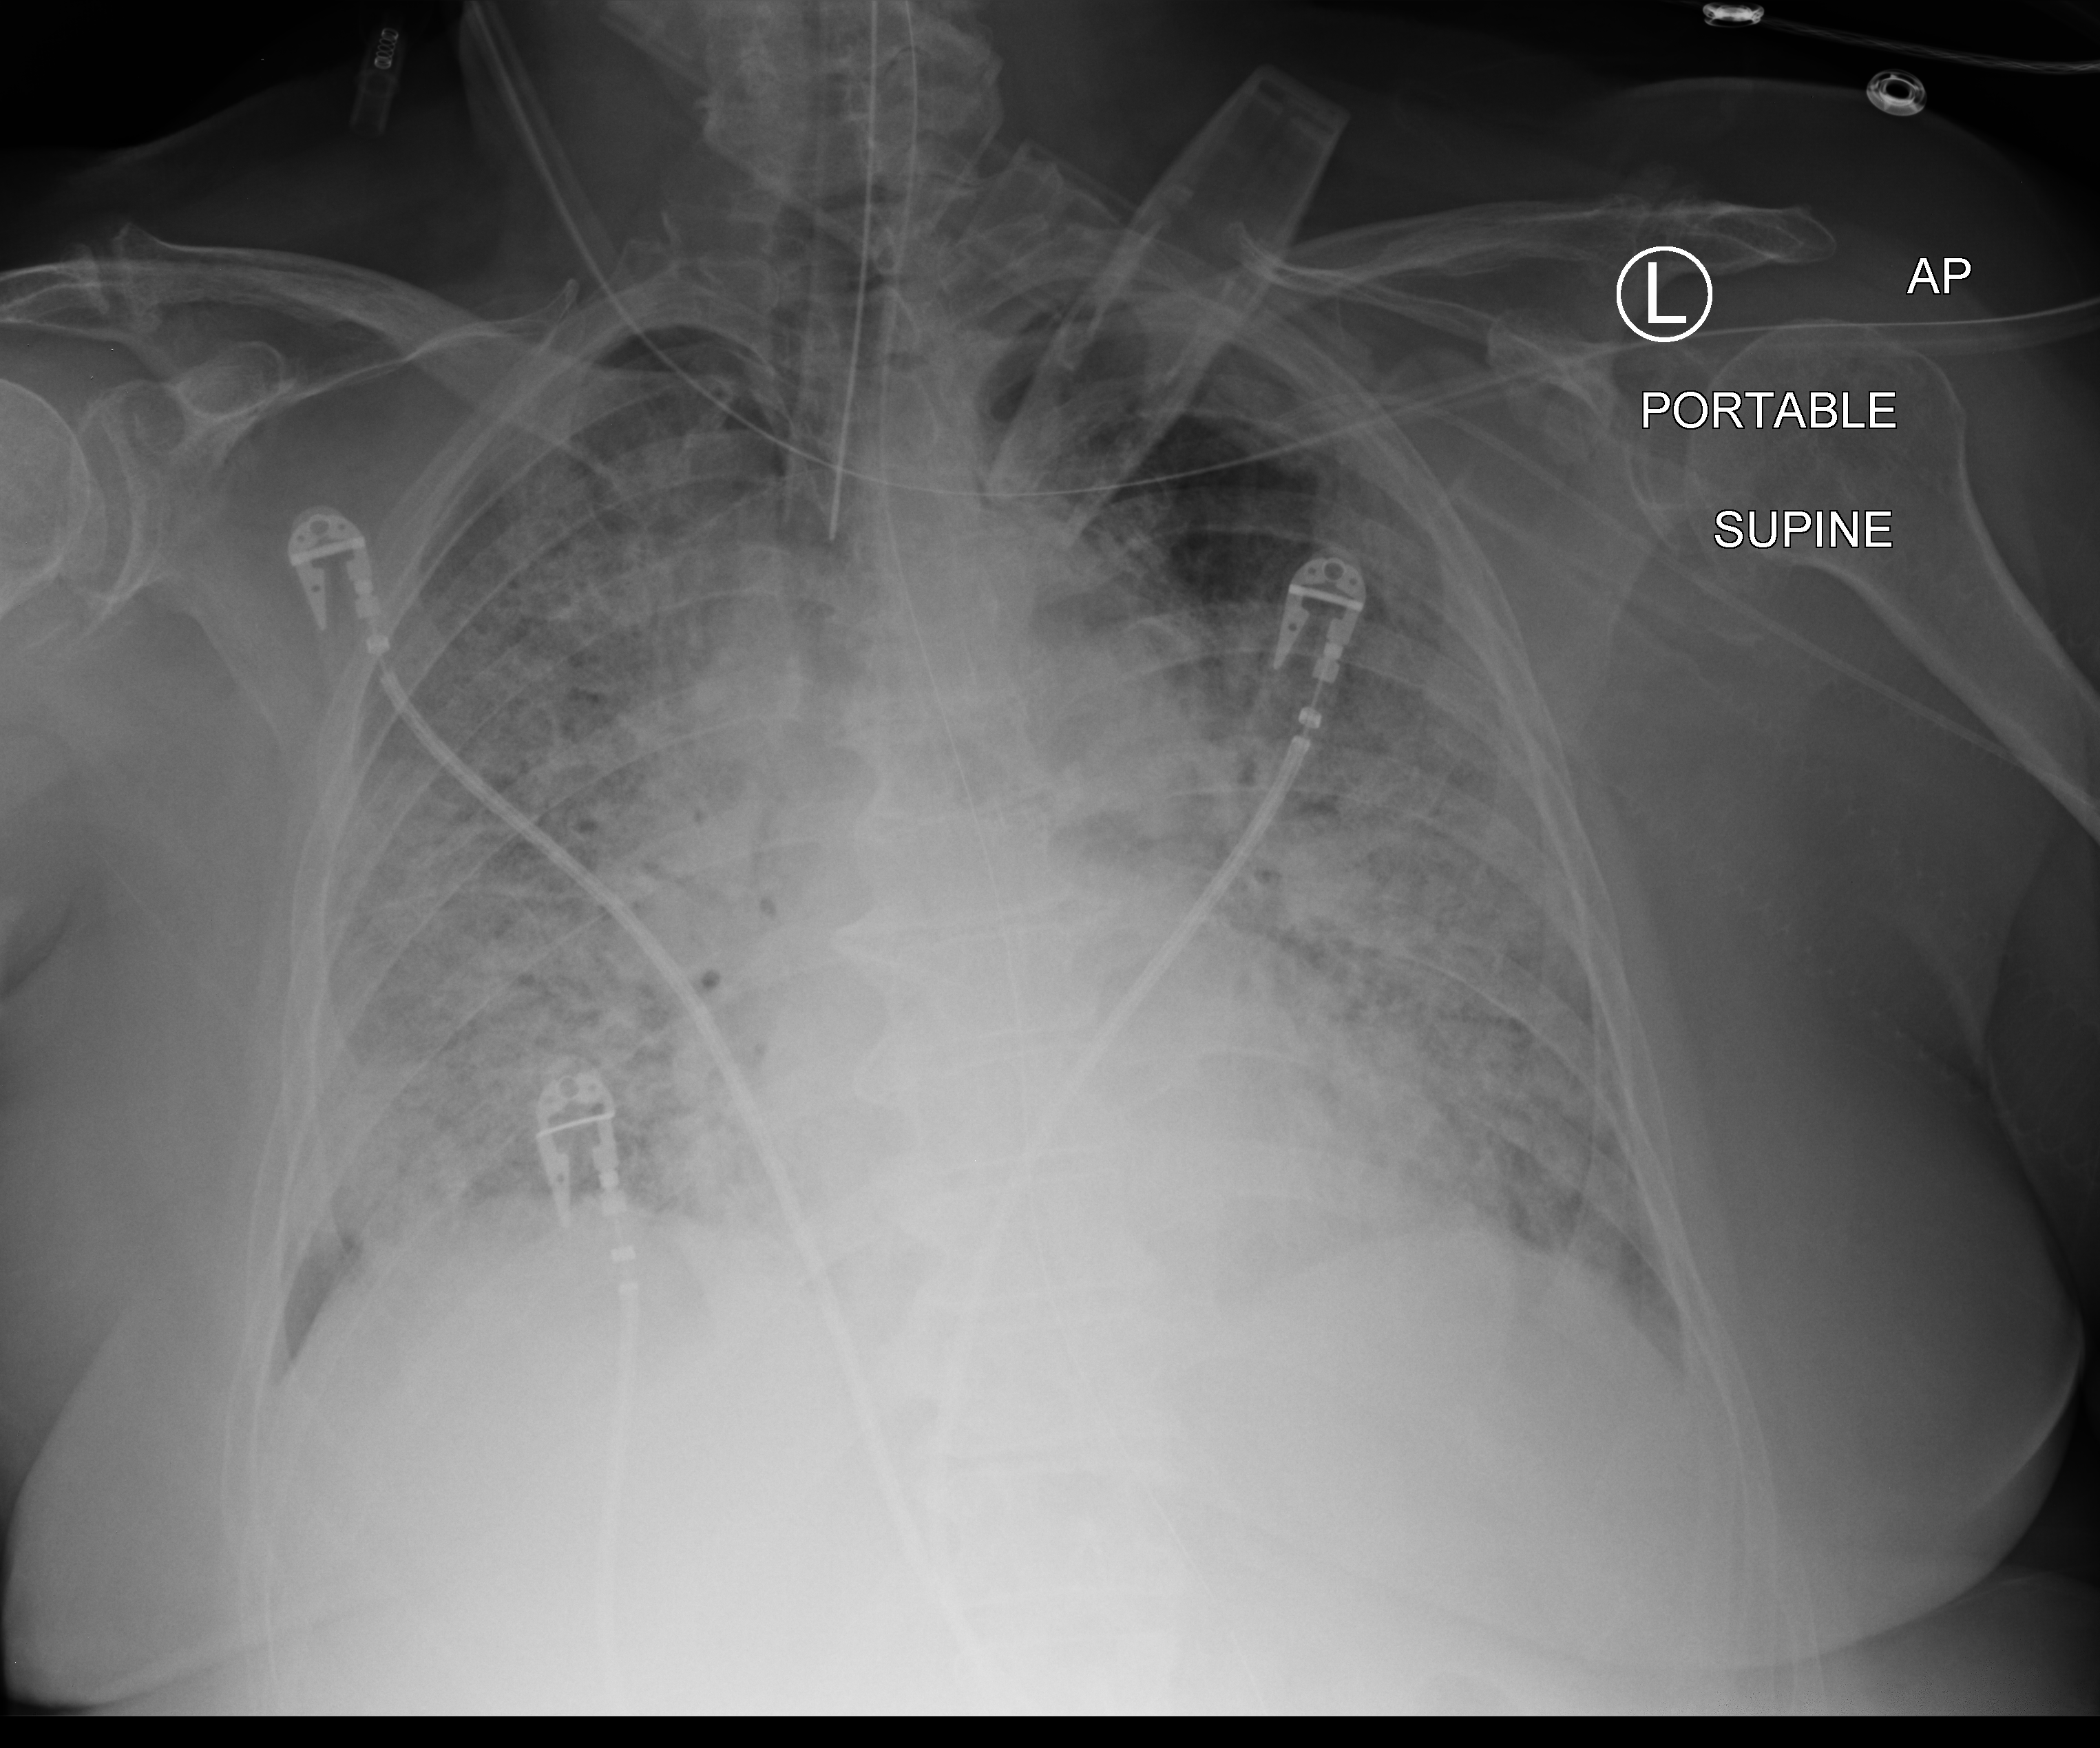
Bedside chest radiograph (computed radiography); anteroposterior (AP) projection. Female patient hospitalised with COVID-19, age 75–90 years.
Admission-level facts for this patient (not findings on this image; timing relative to this image not recorded): mechanically ventilated during this hospital stay: yes; COPD (admission record): no; admitted to intensive care during this hospital stay: no.